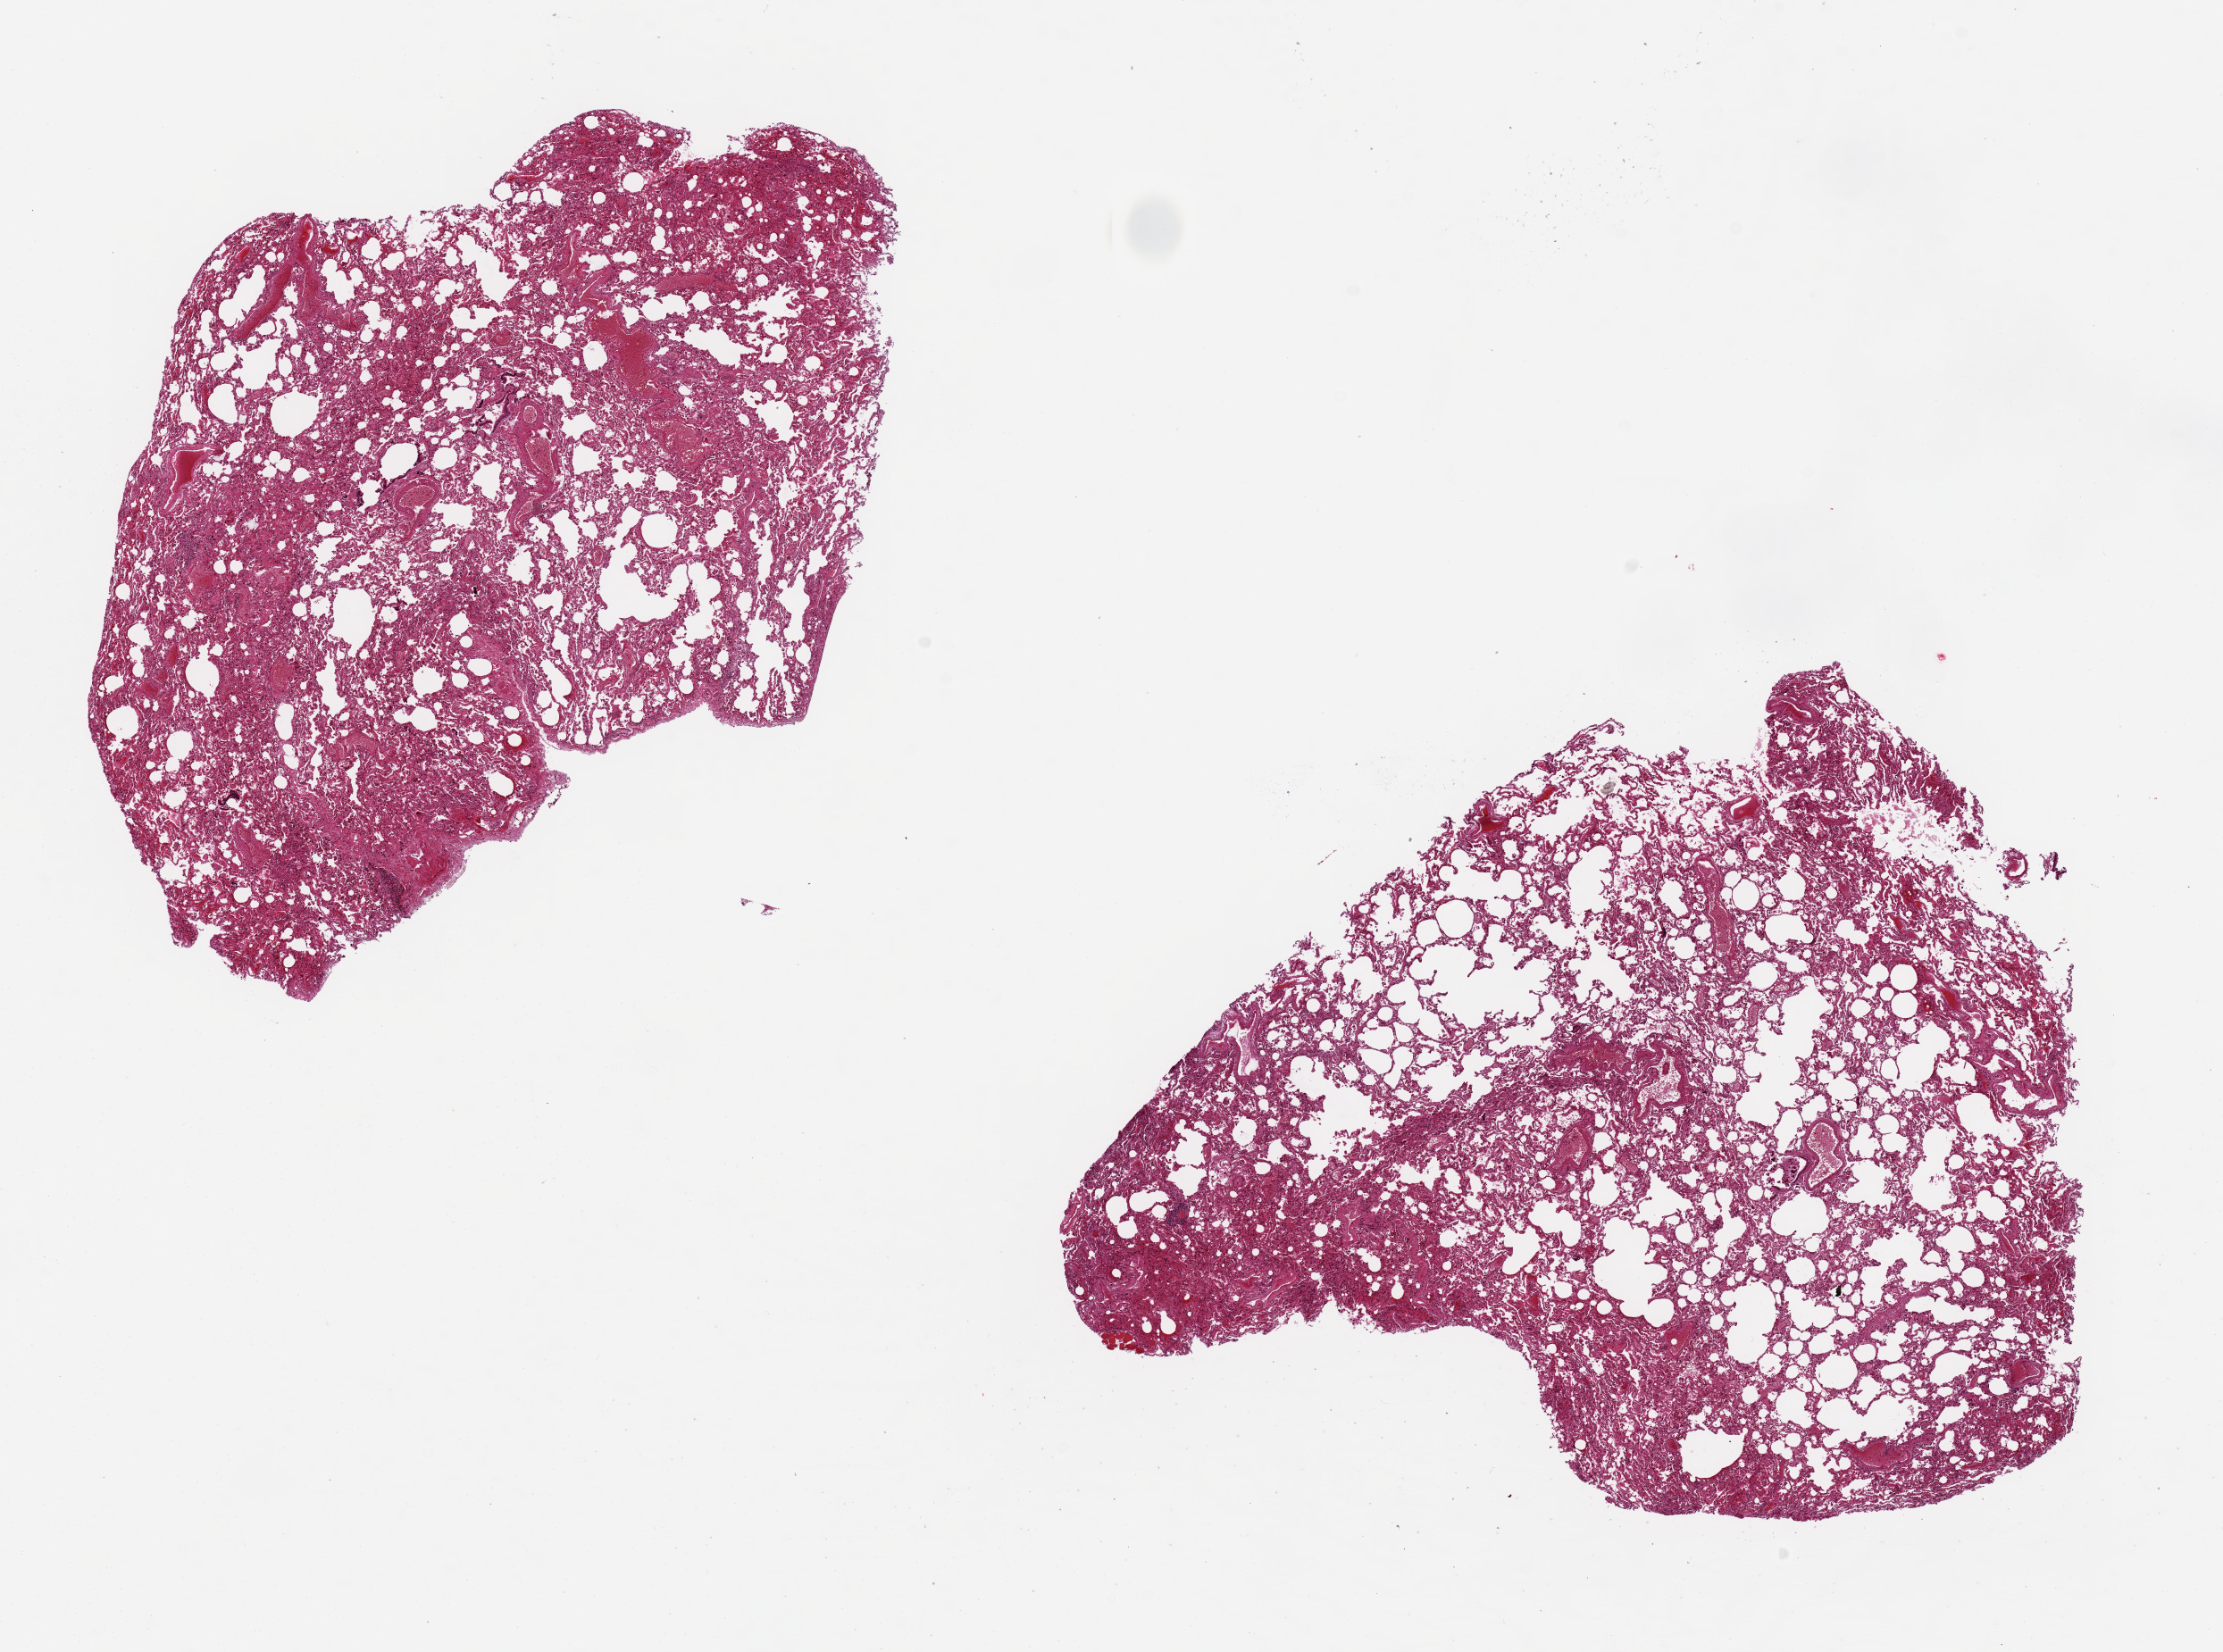
Whole-slide image, hematoxylin and eosin (H&E) stain, brightfield — a low-resolution overview of the entire scanned area, about 19.7 x 14.6 mm (acquisition: 20x scan). PAXgene-fixed paraffin-embedded (PFPE) section. Target tissue: lung. Donor tissue sample.
Pathologist's review note for this sample: 2 aliquots, ~ 7.5x7.5mm, badly autolyzed, moderate congestion.